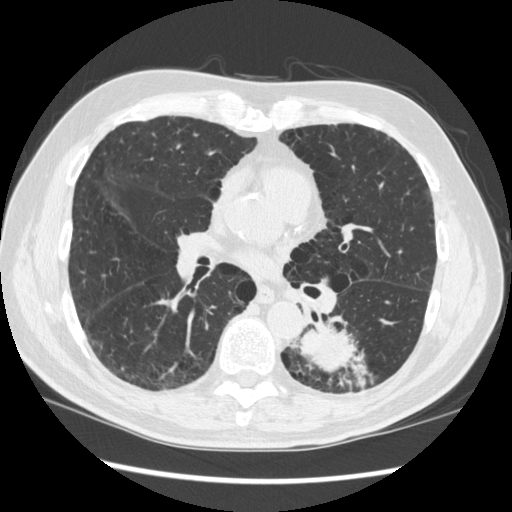
Axial slice from a low-dose chest CT screening exam. First (baseline) screen. Lung window (W 1500 / L -600 HU). 120 kVp. Male, age 72 years at enrolment. Current smoker at enrolment.
Expert reader's lesion annotation, bounding box (x1, y1, x2, y2) in pixels: (265, 306, 369, 399). The screening reader recorded 2 non-calcified nodules or masses ≥4 mm on this exam (left lower lobe, right middle lobe); which of them this box marks is not recorded. Participant outcome: lung cancer diagnosed 37 days after this screen — squamous cell carcinoma, NOS, left lower lobe, stage IIIA (AJCC 6th edition), 60 mm at pathology.